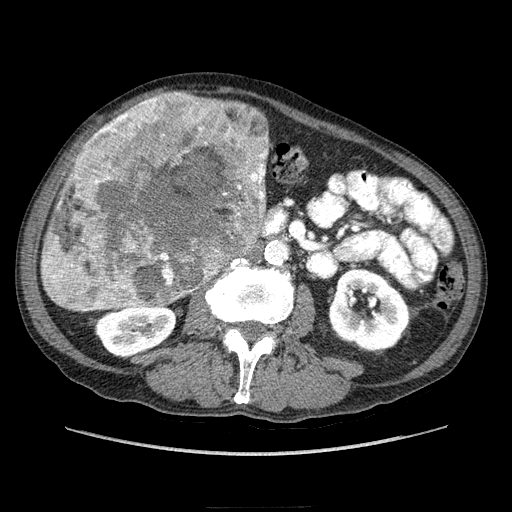
Contrast-enhanced abdominal CT (liver protocol), one axial slice. Position 79 of 218 along the scan axis. Soft-tissue window (W 400 / L 40 HU). 512 × 512 image matrix. From the clinical record (not read from this slice): diagnosis: hepatocellular carcinoma (patient treated with transarterial chemoembolisation; whether this scan precedes or follows treatment is not stated here); TNM stage (as recorded): Stage-IIIA; Child-Pugh class: A; tumour differentiation: well differentiated; tumour nodularity: multinodular.
Outlined on this slice (semi-automatic segmentation, software-assisted and operator-edited):
- liver parenchyma outside the tumour (the mass and vessels are separate outlines, so this box may not span the whole liver): bounding box <40,139,90,312> (left, top, right, bottom; pixels)
- mass: <41,91,270,311>